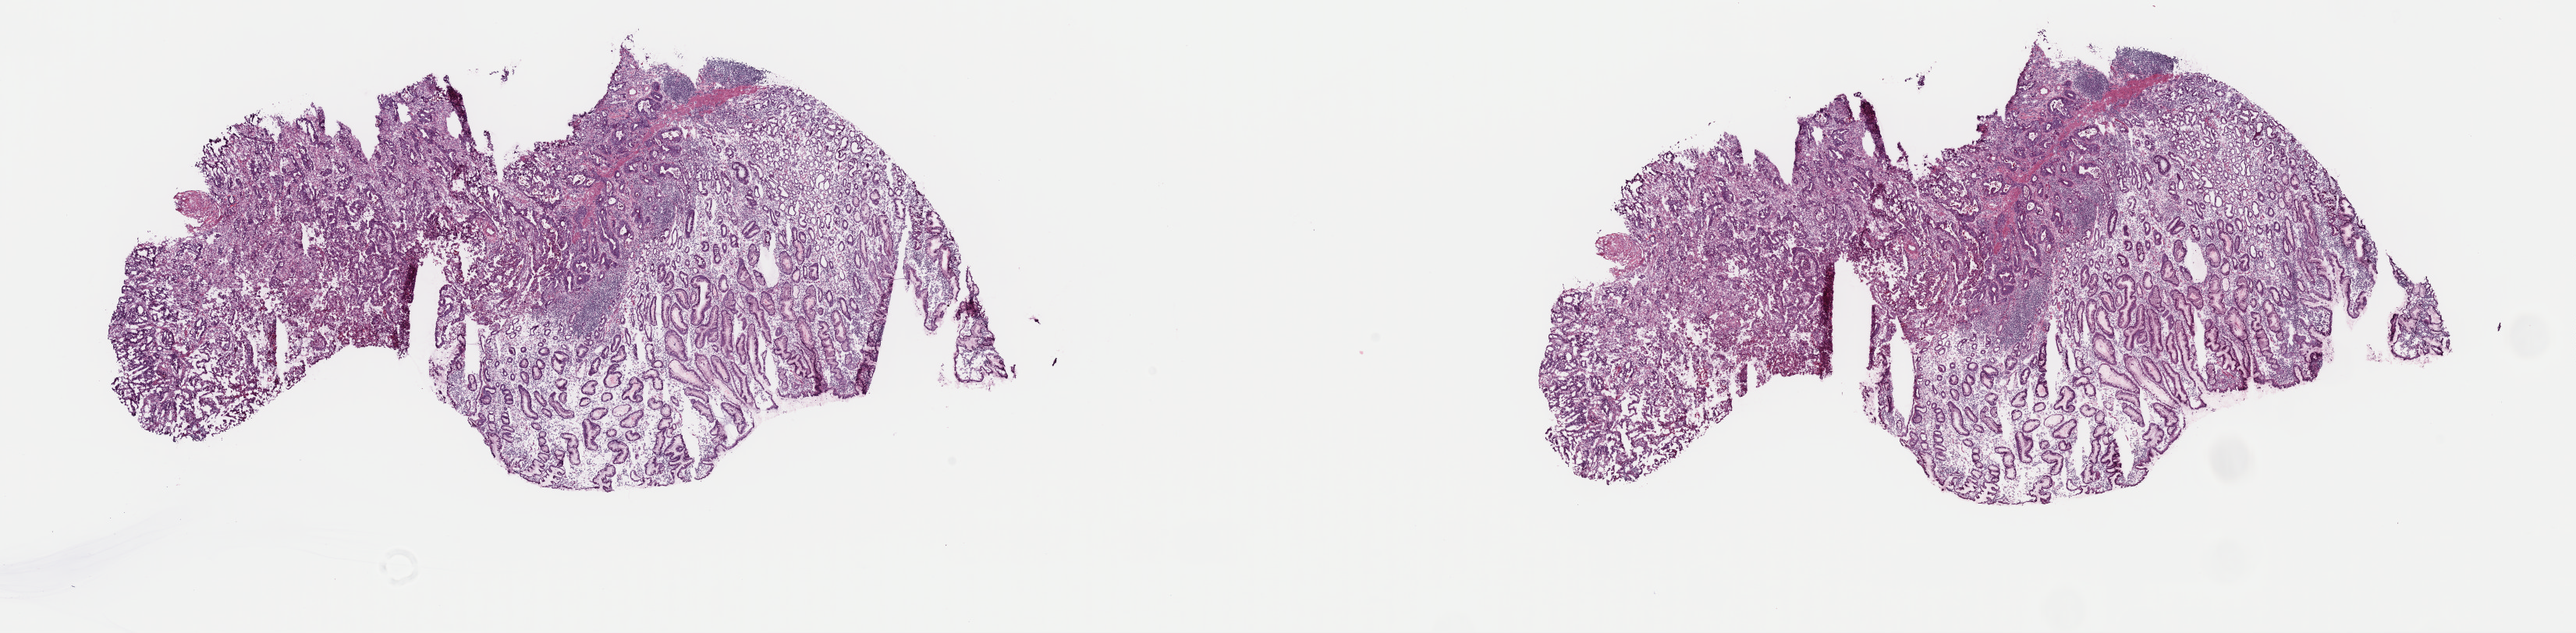
Digitized Hematoxylin and eosin (H&E) stained tissue section (whole slide), low-resolution overview of the scanned area, about 26.1 x 6.4 mm, frozen section from the top of the tissue portion, primary tumour sample from the stomach. Patient: male, age at initial diagnosis 68 years. Histologic grade: G2 (moderately differentiated). Pathologist review of this section (percent, as recorded): tumour cells 80%, tumour nuclei 80%, normal cells 0%, stromal cells 10%, necrosis 10%. Infiltration values recorded for this section: lymphocyte infiltration 40%, monocyte infiltration 20%, neutrophil infiltration 20%.
• lymph nodes positive (case pathology): 0 of 13 examined
• pathologic diagnosis: Adenocarcinoma, intestinal type
• AJCC pathologic stage: IIA